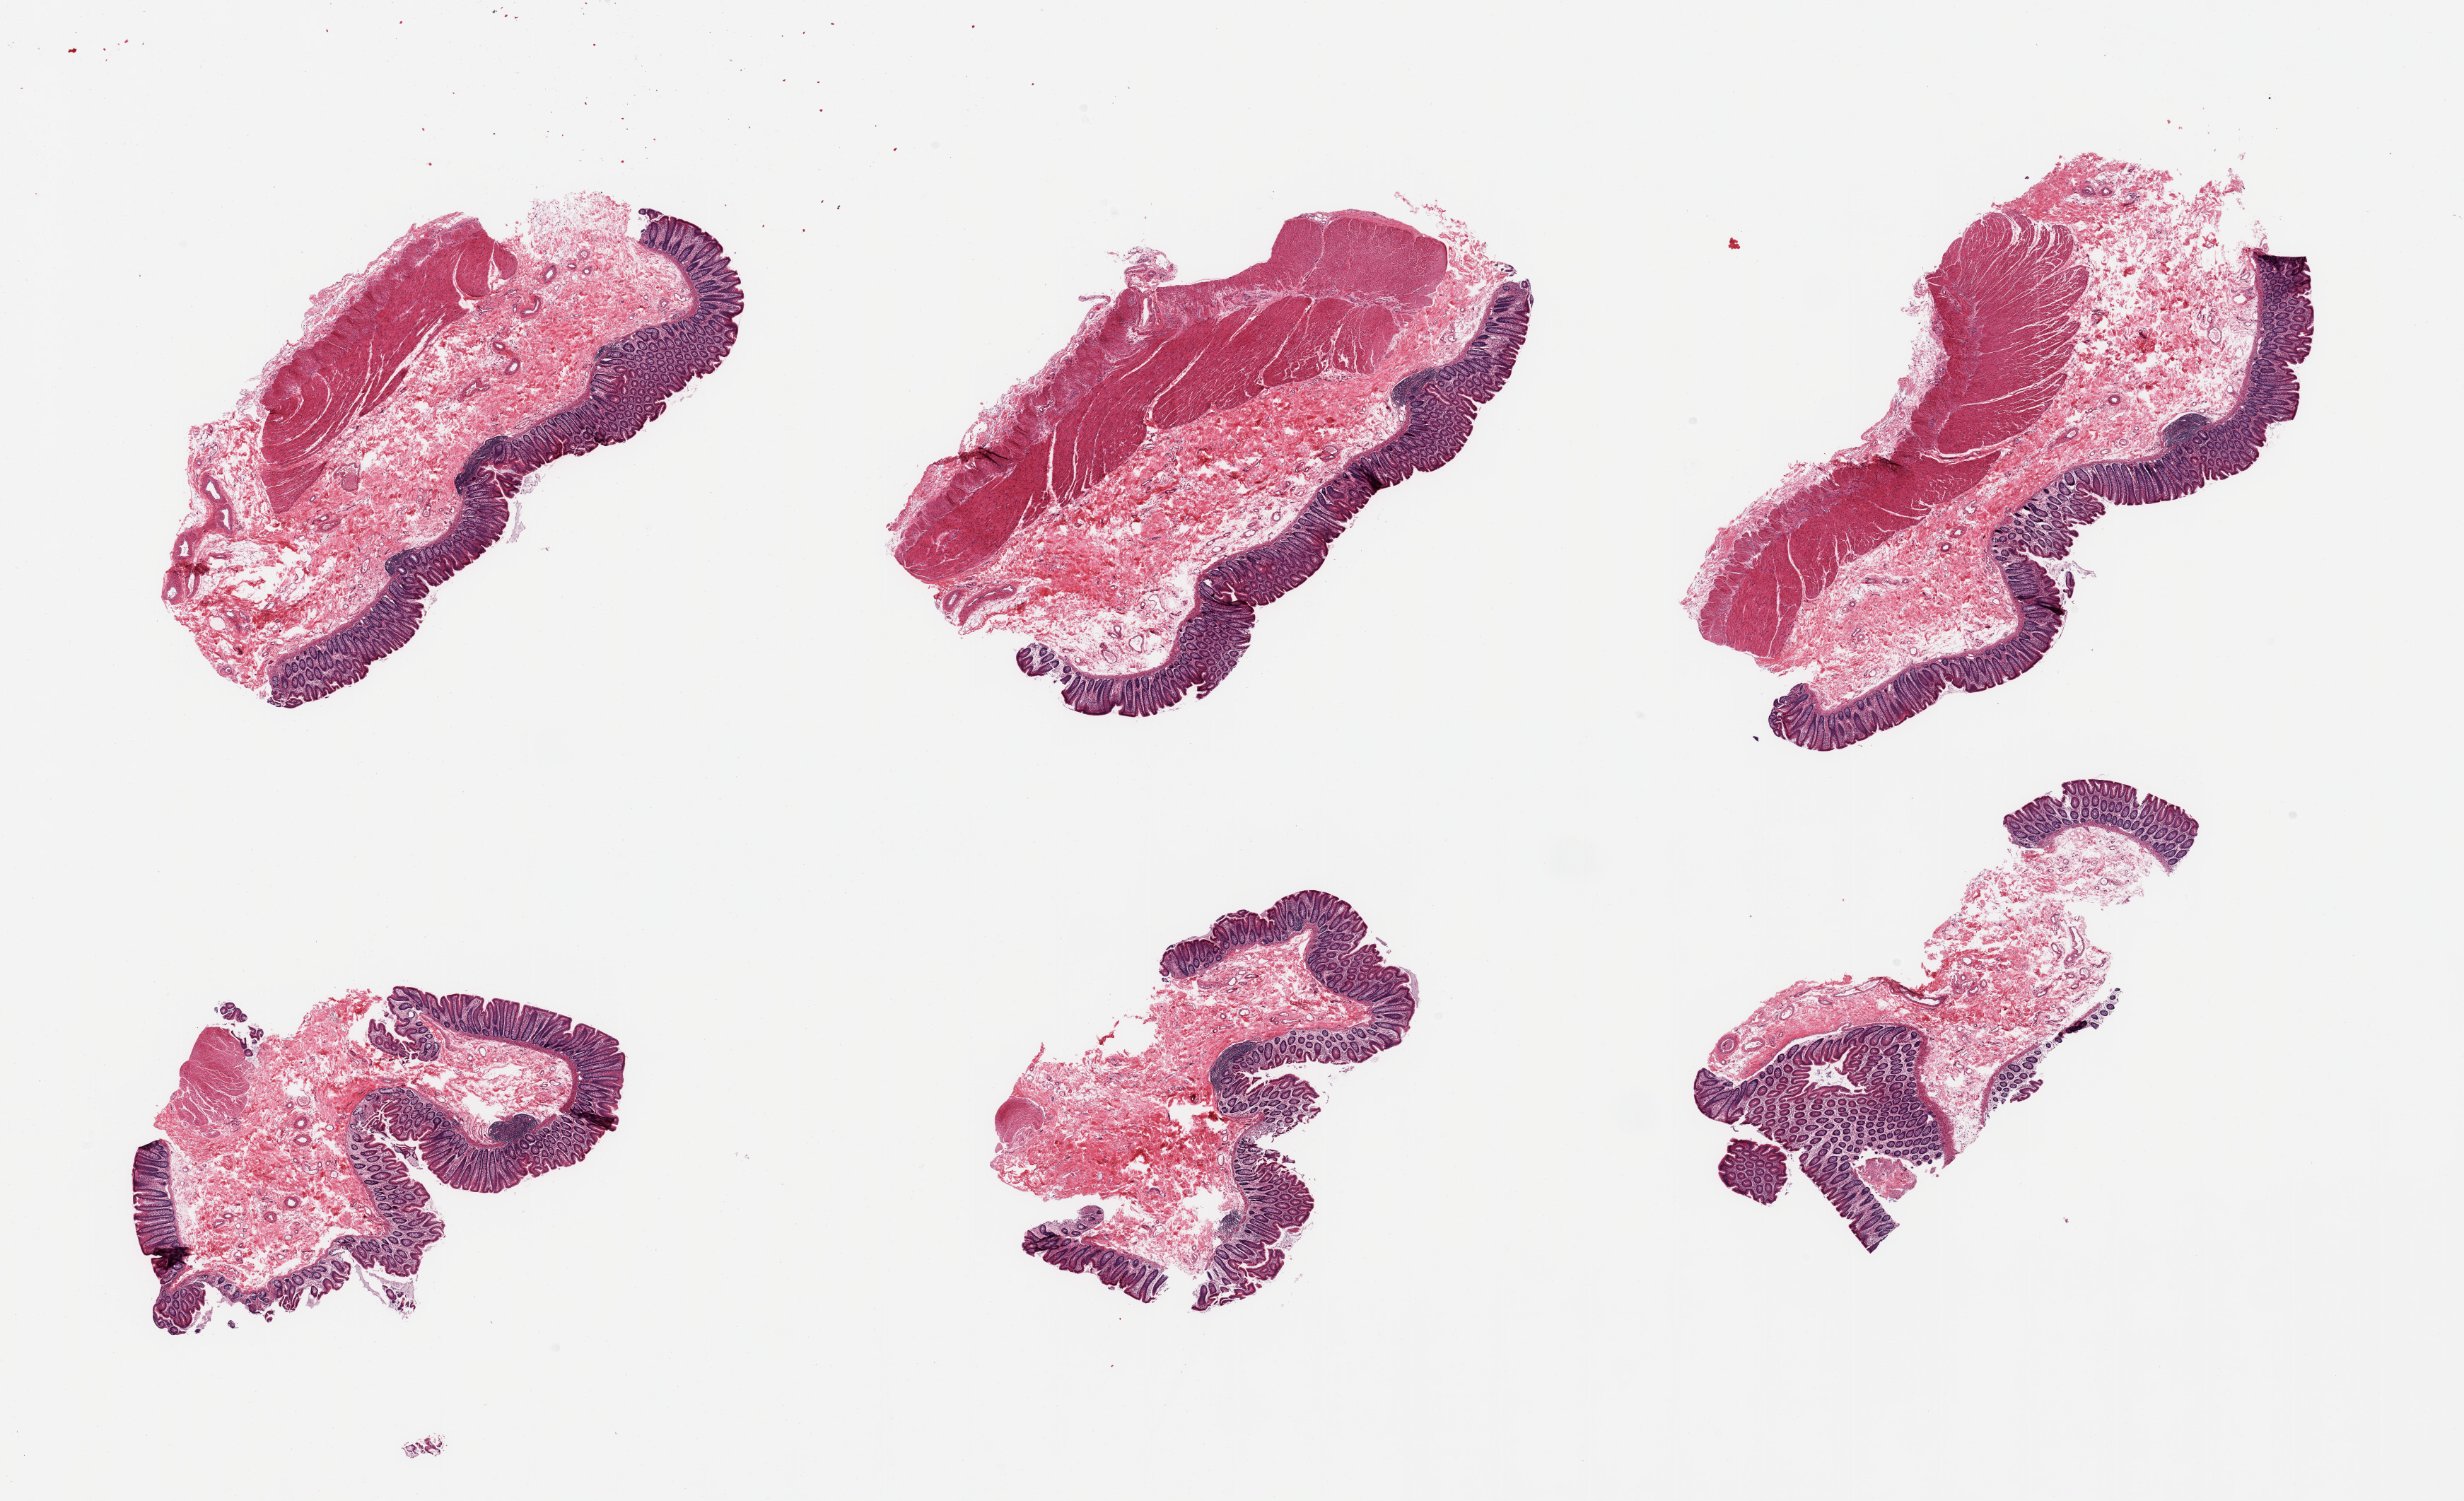
Hematoxylin and eosin (H&E) whole-slide image, brightfield — whole scanned area (about 27.6 x 16.8 mm, acquisition: 20x scan) shown as a low-resolution overview, PAXgene-fixed paraffin-embedded (PFPE) section, target tissue: transverse colon, donor tissue sample.
Reviewer comment on this tissue sample: 6 pieces, mucosa well- preserved up to ~0.5-1mm.